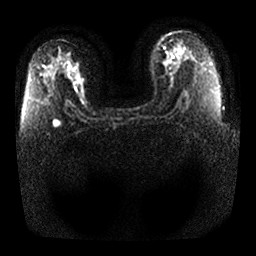
Breast MRI, one axial slice. Position 17 of 25 along the scan axis. Diffusion-weighted series; image 2 of 4 stored at this slice position (different b-values; order by instance number). 1.5 T. 4 mm slice thickness. 256 × 256 image matrix, field of view 350 × 350 mm. Female patient.
Outlined on this slice (expert manual segmentation):
- tumour on diffusion-weighted imaging: bounding box <76,76,86,104> (left, top, right, bottom; pixels)